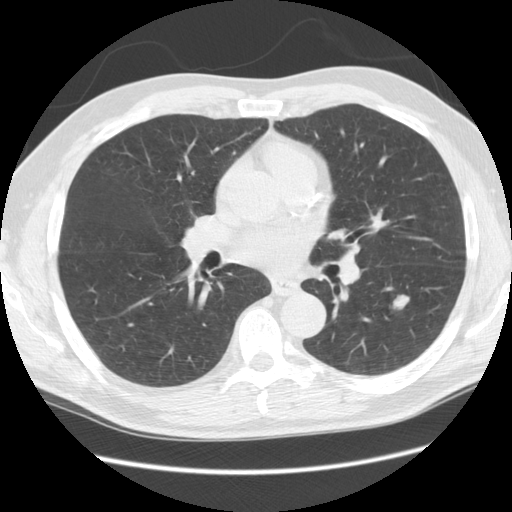
Chest CT (low-dose screening protocol), one axial image; third annual screen; lung window (W 1500 / L -600 HU); 2.5 mm slice thickness; slice 57 of 111 in the series. Male, age 60 years at enrolment.
- Expert reader's lesion annotation, bounding box (x1, y1, x2, y2) in pixels: (382, 289, 416, 319).
- The screening reader recorded 5 non-calcified nodules or masses ≥4 mm on this exam (left lower lobe, right lower lobe, right lower lobe, left lower lobe, left upper lobe); which of them this box marks is not recorded.
- Official screen result: positive, other.